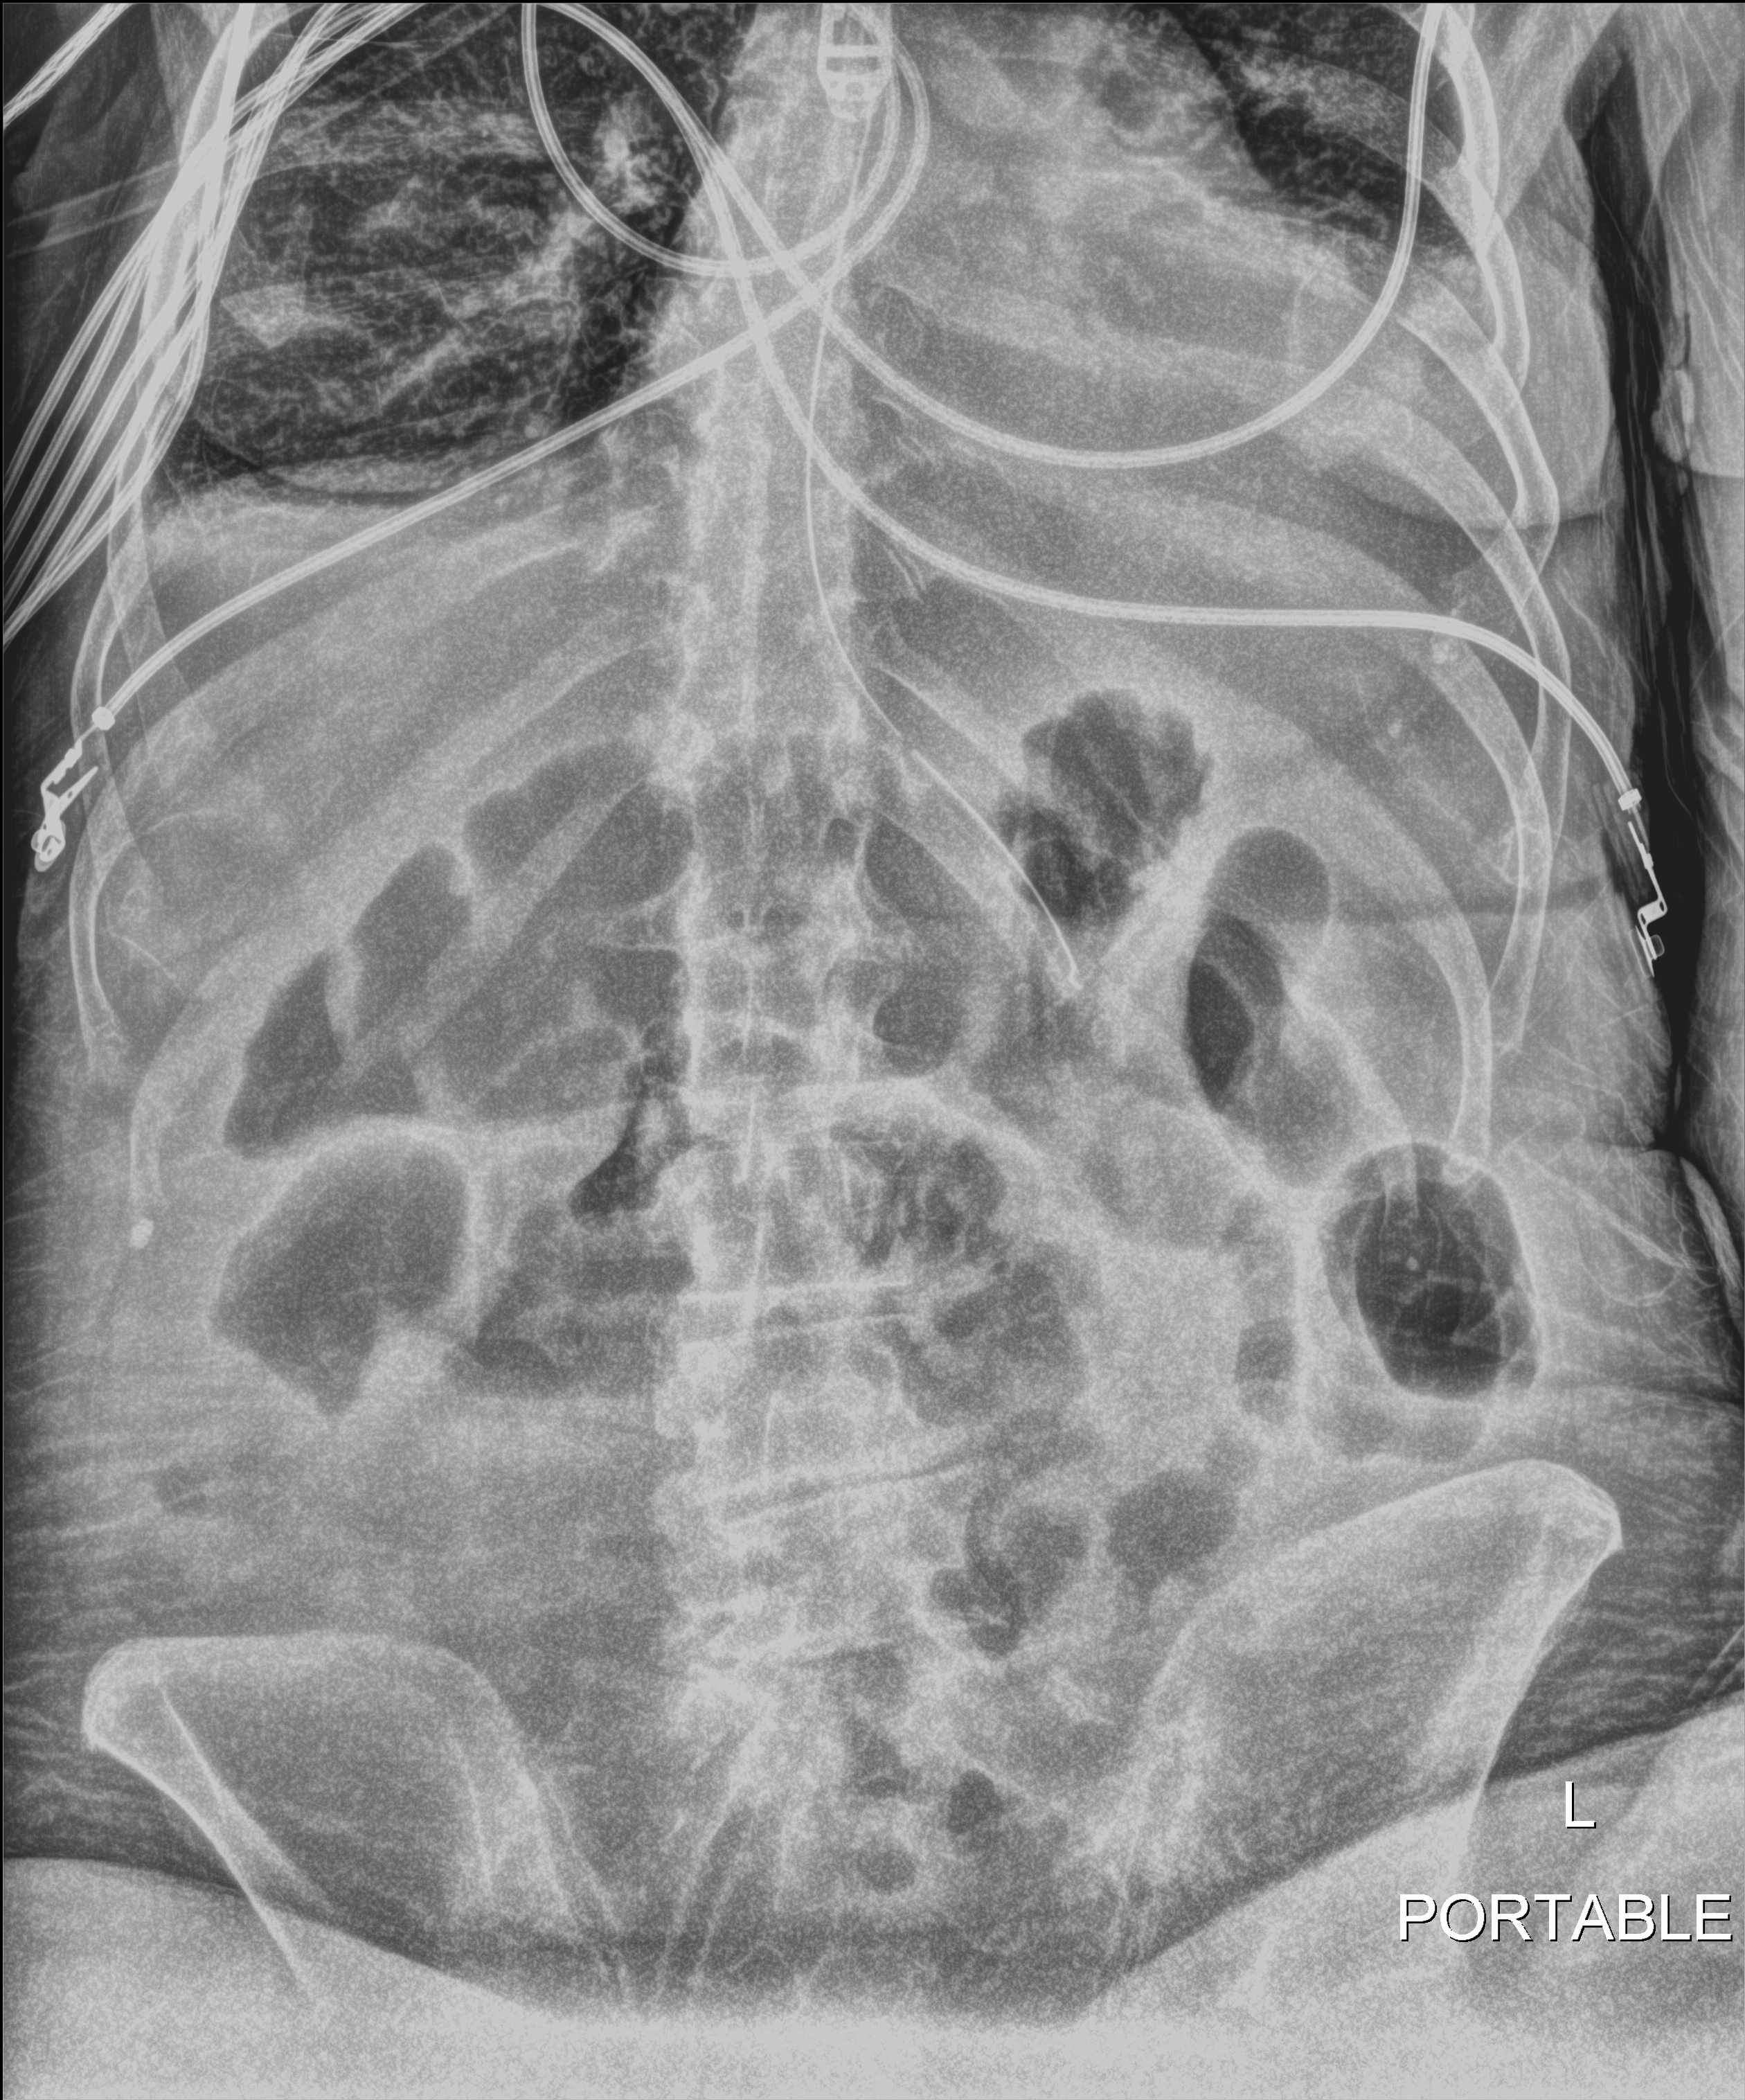
Bedside abdomen radiograph (digital radiography), anteroposterior (AP) projection. Female patient hospitalised with COVID-19, age 60–74 years.
Admission-level facts for this patient (not findings on this image; timing relative to this image not recorded):
- admitted to intensive care during this hospital stay: yes
- mechanically ventilated during this hospital stay: yes